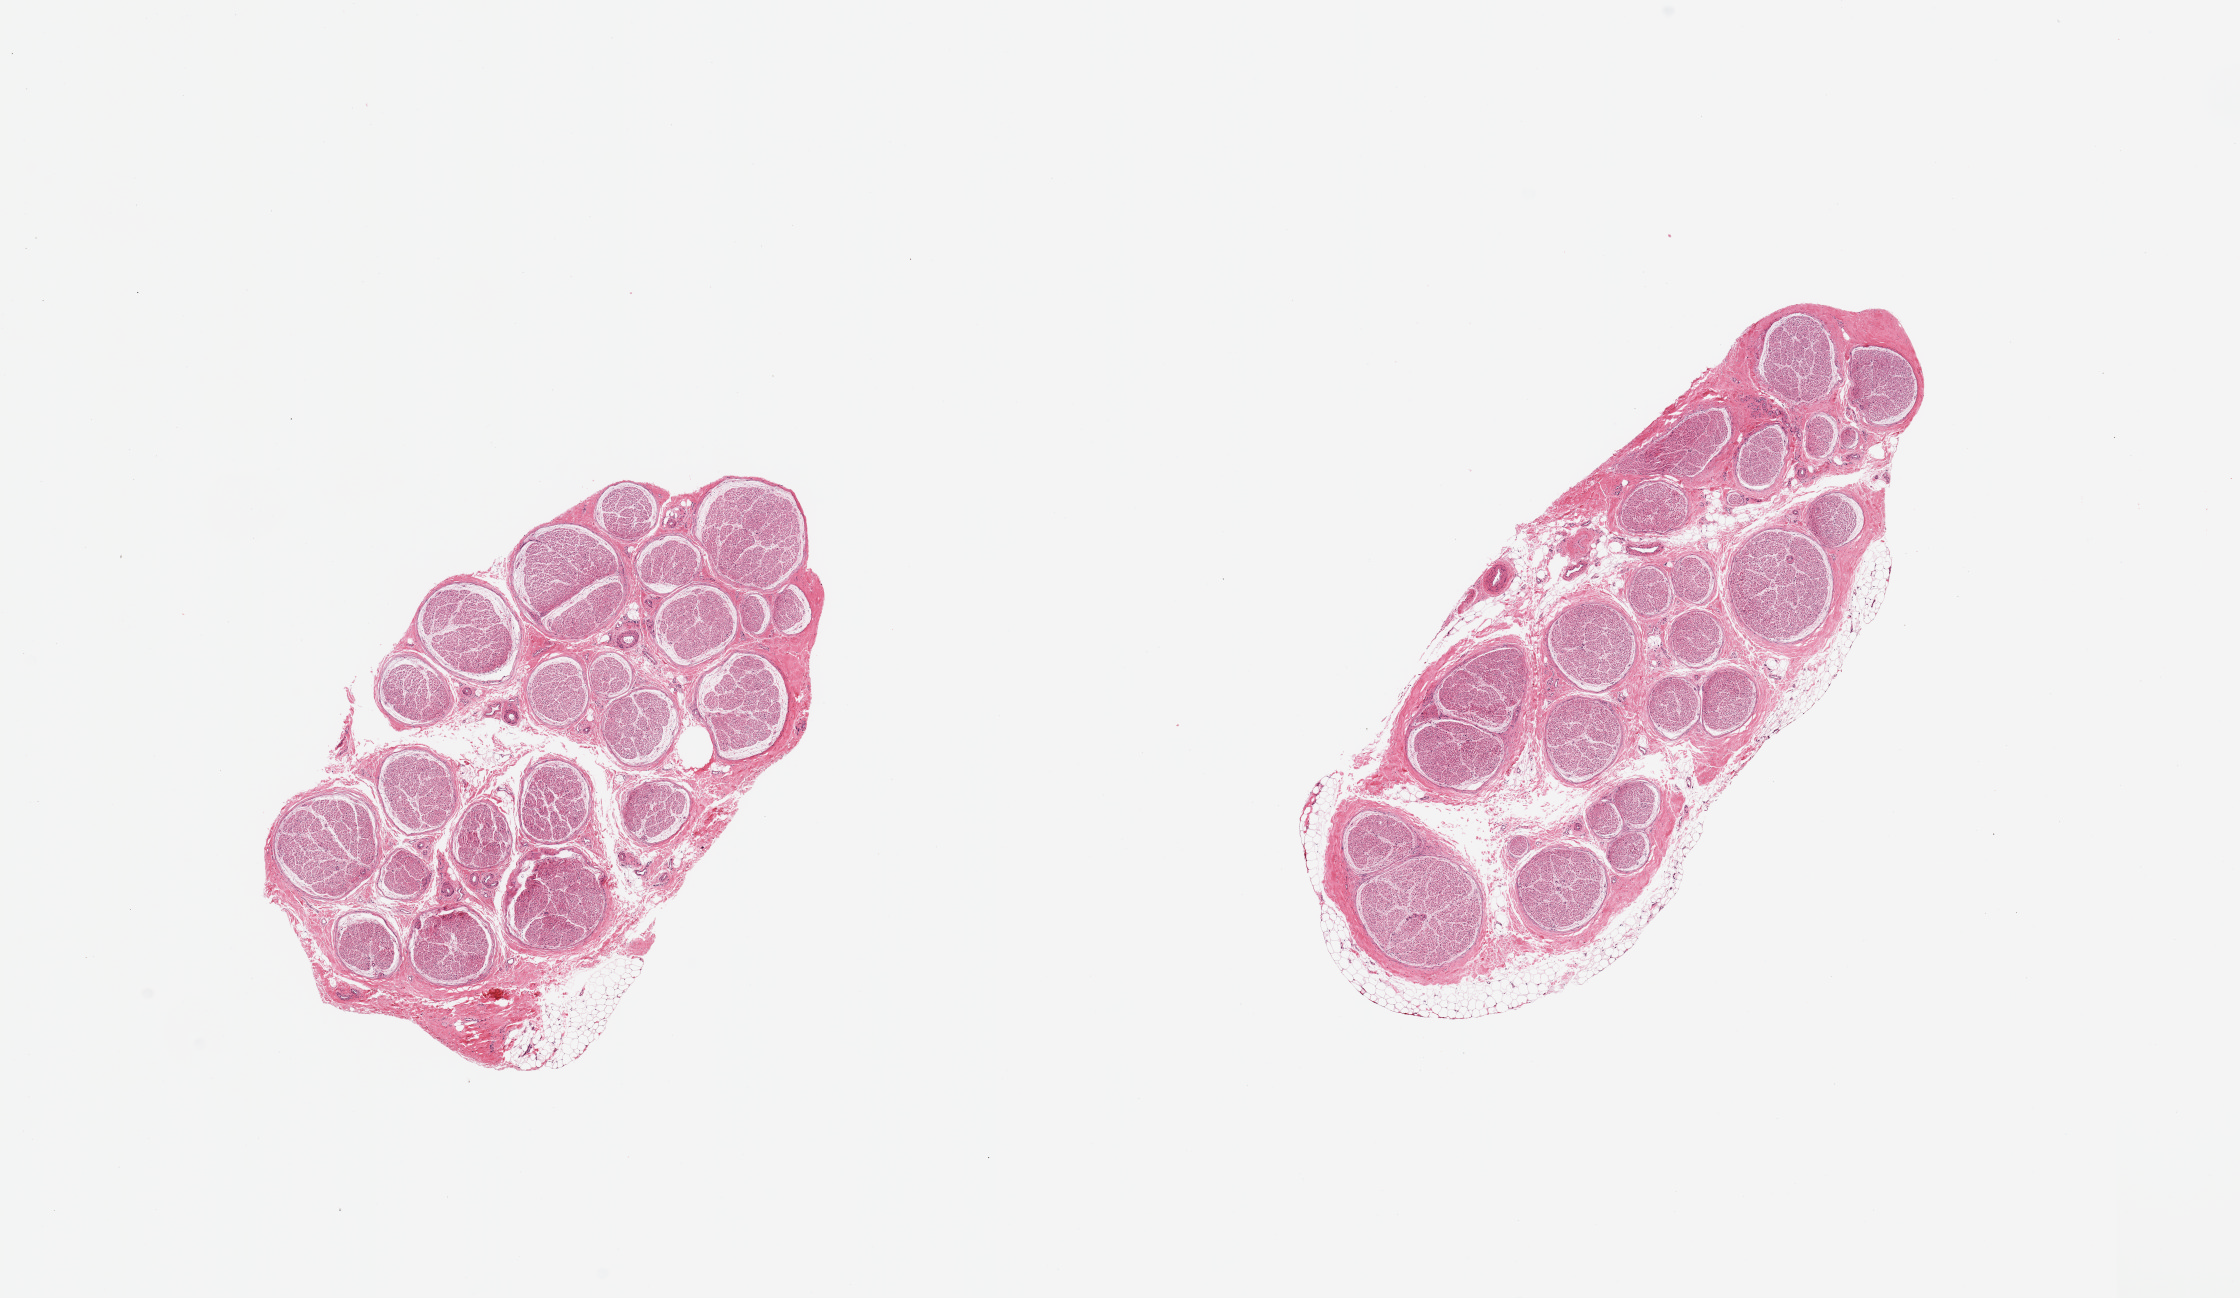
H&E whole-slide image, brightfield, low-resolution overview of the scanned area, about 17.7 x 10.3 mm (slide scanned at 20x); PAXgene-fixed, paraffin-embedded tissue; section of tibial nerve (target tissue); donor tissue sample. Female donor.
Reviewer comment on this tissue sample: 2 pieces, trace adherent fat.